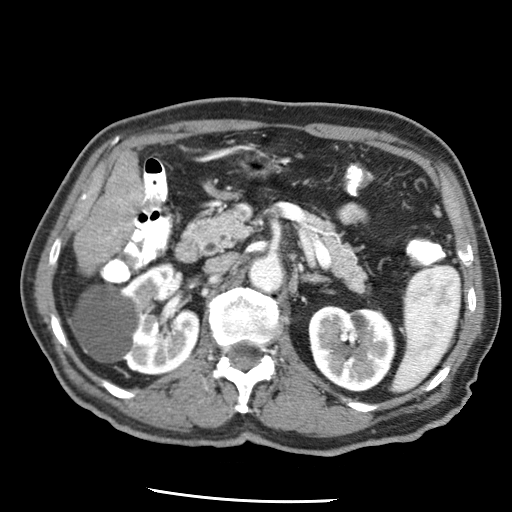
Contrast-enhanced abdominal CT (liver protocol), one axial slice; slice 14 of 79 in the series (ordered by position); reconstruction kernel STANDARD; 120 kVp; soft-tissue window (W 400 / L 40 HU); 2.5 mm slice thickness; 512 × 512 image matrix, field of view 320 × 320 mm. From the clinical record (not read from this slice): diagnosis: hepatocellular carcinoma (patient treated with transarterial chemoembolisation; whether this scan precedes or follows treatment is not stated here); TNM stage (as recorded): Stage-IIIA.
Outlined on this slice (semi-automatically segmented with operator editing):
- liver parenchyma outside the tumour (the mass and vessels are separate outlines, so this box may not span the whole liver): bounding box (x1, y1, x2, y2) in pixels: (102, 152, 140, 214)
- liver vessels: (132, 194, 135, 197)